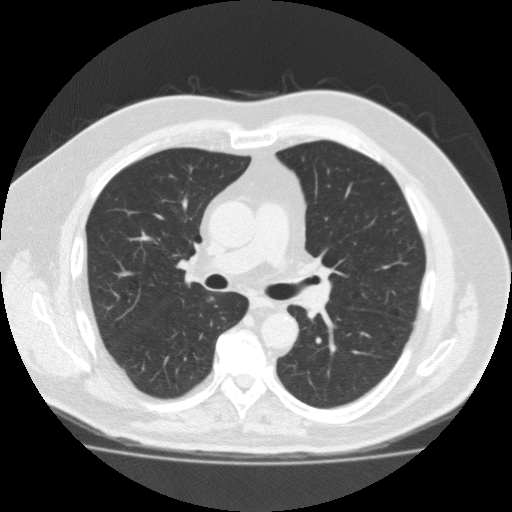
Axial slice from a low-dose chest CT screening exam, third screening round (two years after baseline), lung window (W 1500 / L -600 HU), 512 × 512 image matrix, field of view 391 × 391 mm. Male participant, aged 56 years at enrolment. Current smoker at enrolment.
- Lesion marked by an expert reader, box from (x=185, y=280) to (x=236, y=321) px.
- Screening reader's record for this exam (one nodule recorded; not confirmed to be the boxed lesion): non-calcified nodule or mass ≥4 mm, right lower lobe, 12 × 8 mm, spiculated (stellate) margins, soft tissue attenuation, pre-existing on the prior screen: yes; interval growth: yes.
- Later outcome: lung cancer diagnosed 49 days after this screen — adenocarcinoma, NOS, right lower lobe, moderately differentiated (G2), stage IA (AJCC 6th edition), 12 mm at pathology.